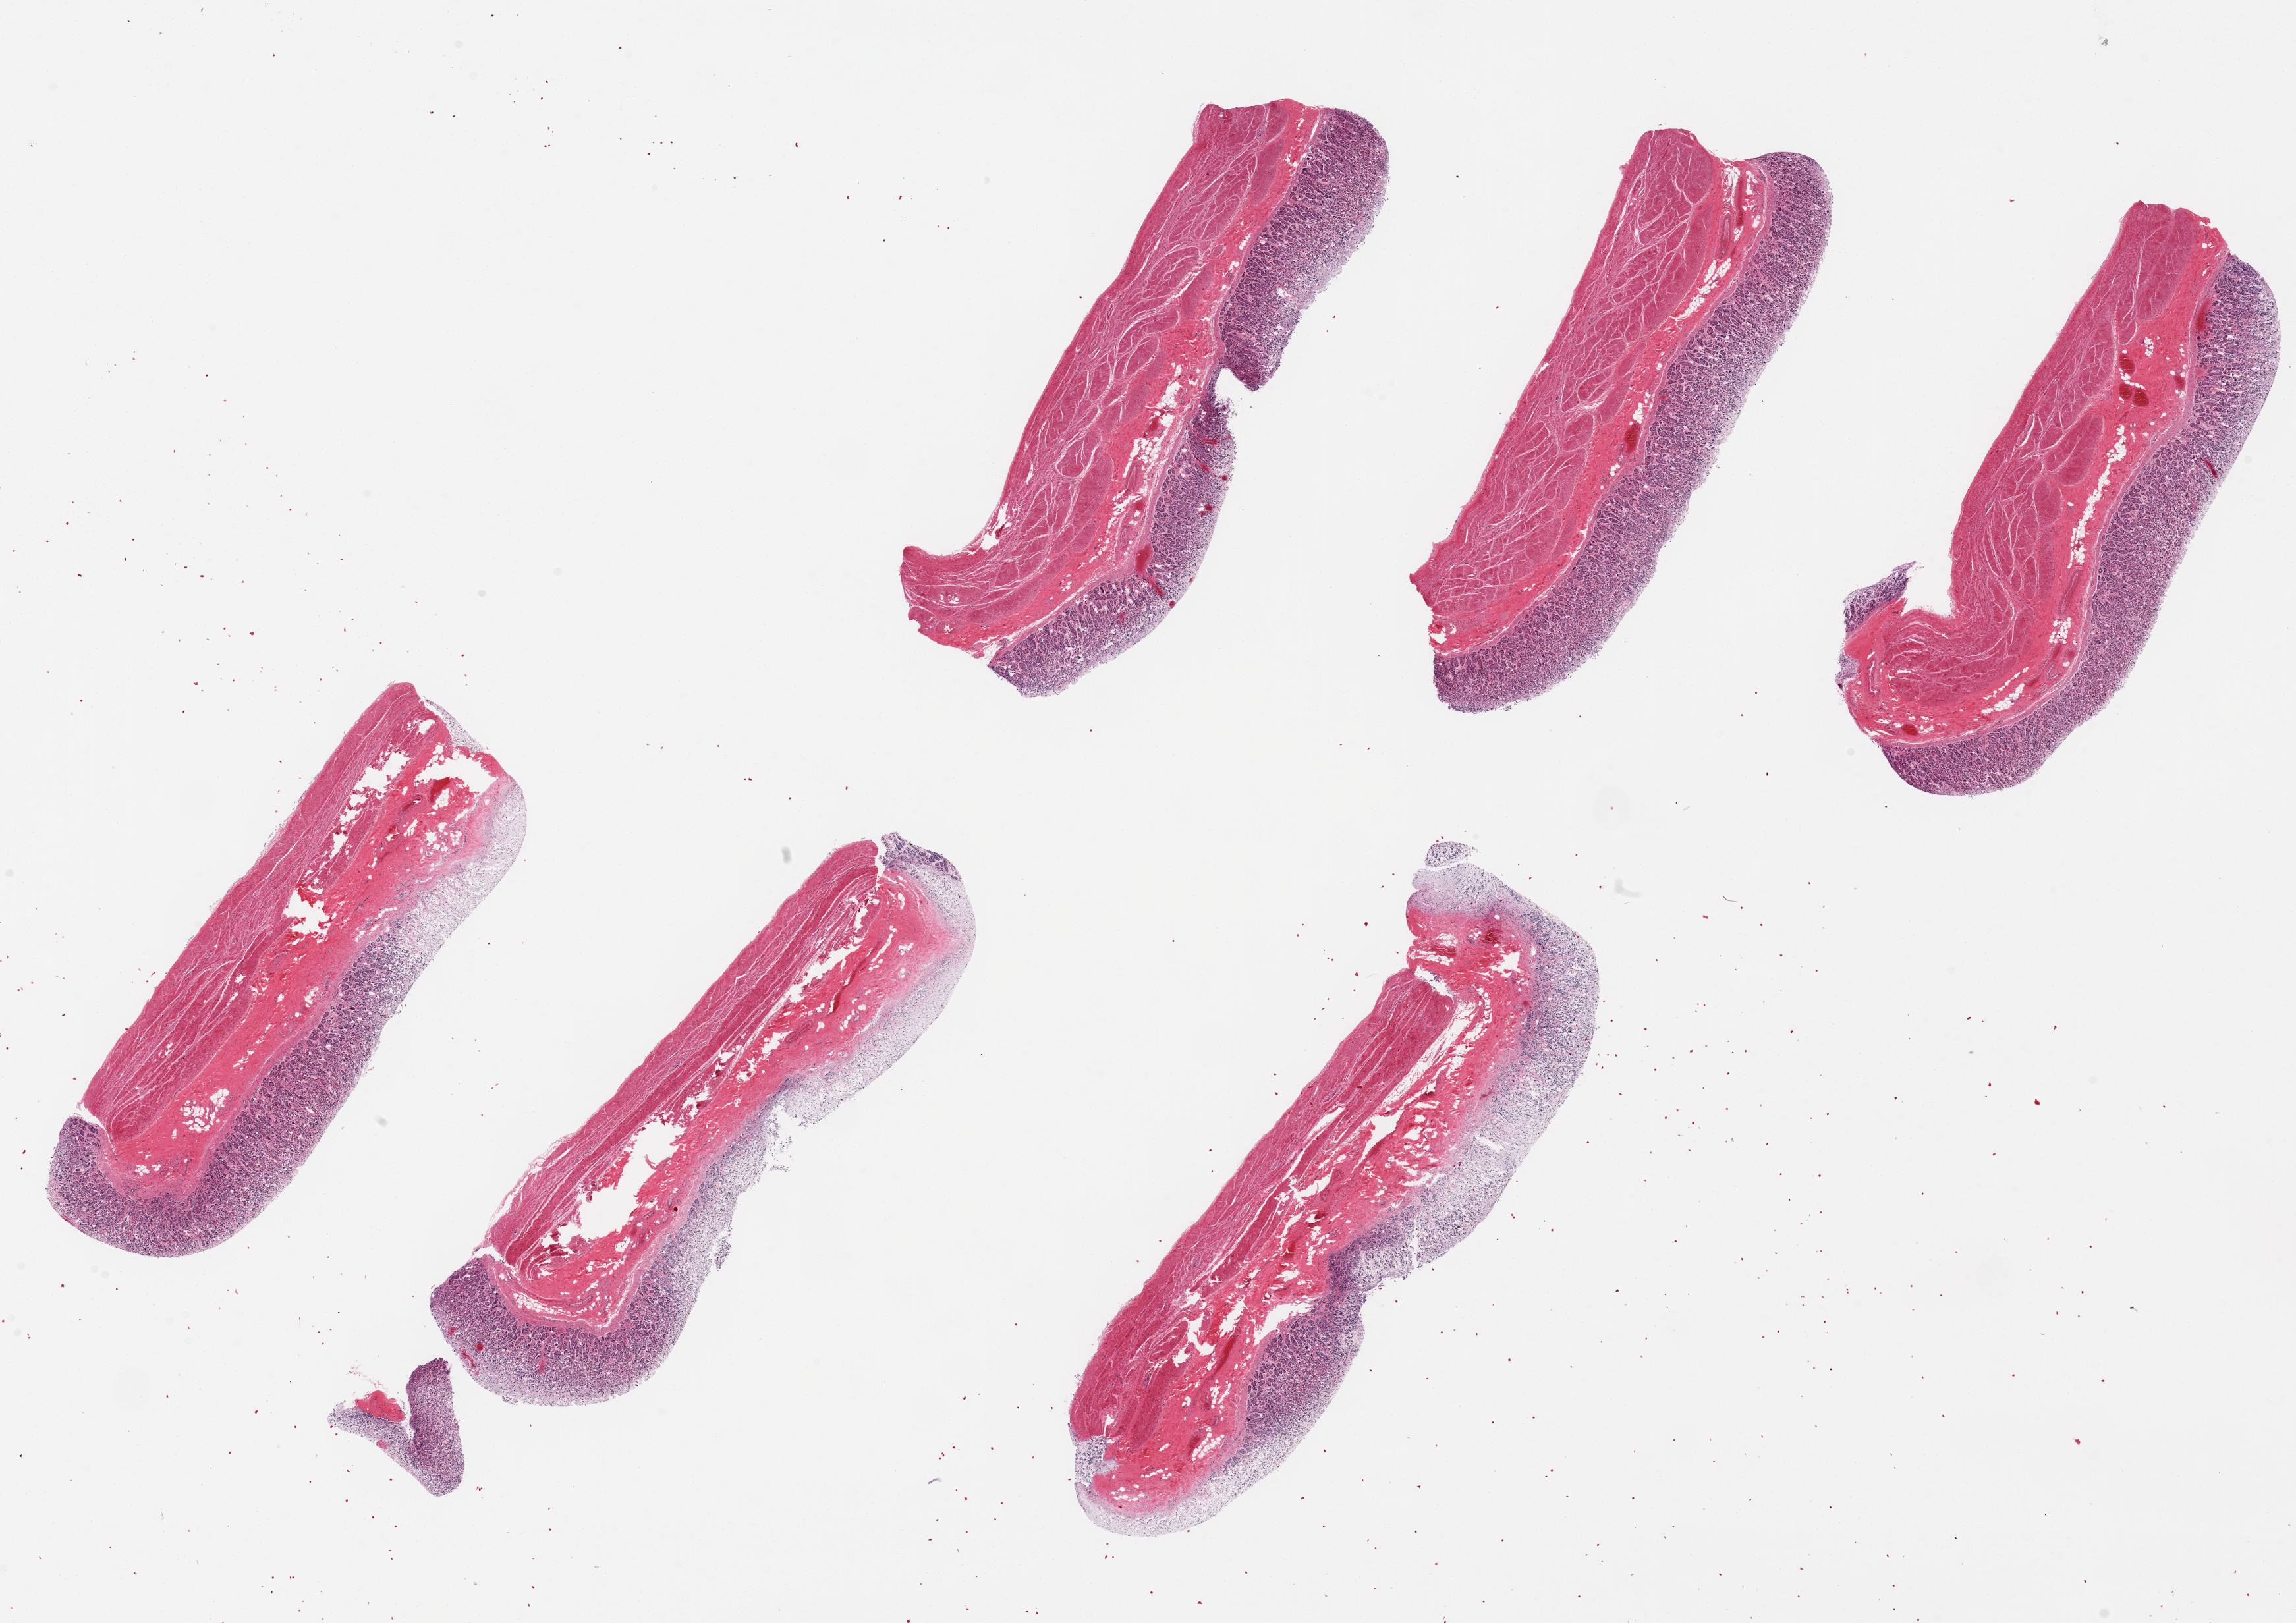
H&E whole-slide image — whole scanned area (about 27.6 x 19.5 mm, slide scanned at 20x) shown as a low-resolution overview; PAXgene-fixed paraffin-embedded (PFPE) section; sampled site (target tissue): stomach; donor tissue sample.
• review note (as recorded): 6 pieces up to 9x2.6 mm; variable mucosal preservation: overall superficial autolysis, several areas of full thickness autolysis; several pieces with sectioning artifacts